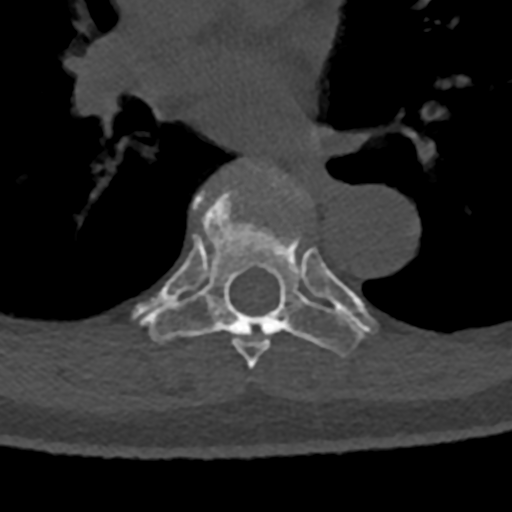
CT including the spine, one axial slice. Reconstruction kernel Br40s/3. 120 kVp. Bone window (W 1800 / L 400 HU). 0.5 mm slice thickness. 512 × 512 image matrix, field of view 160 × 160 mm. Male patient, age 74 years. From the clinical record (not read from this slice): primary cancer: renal.
Outlined on this slice (semi-automatically segmented with operator editing):
- T6 vertebra: bounding box (x1, y1, x2, y2) in pixels: (185, 191, 270, 369)
- T7 vertebra: (133, 180, 374, 355)